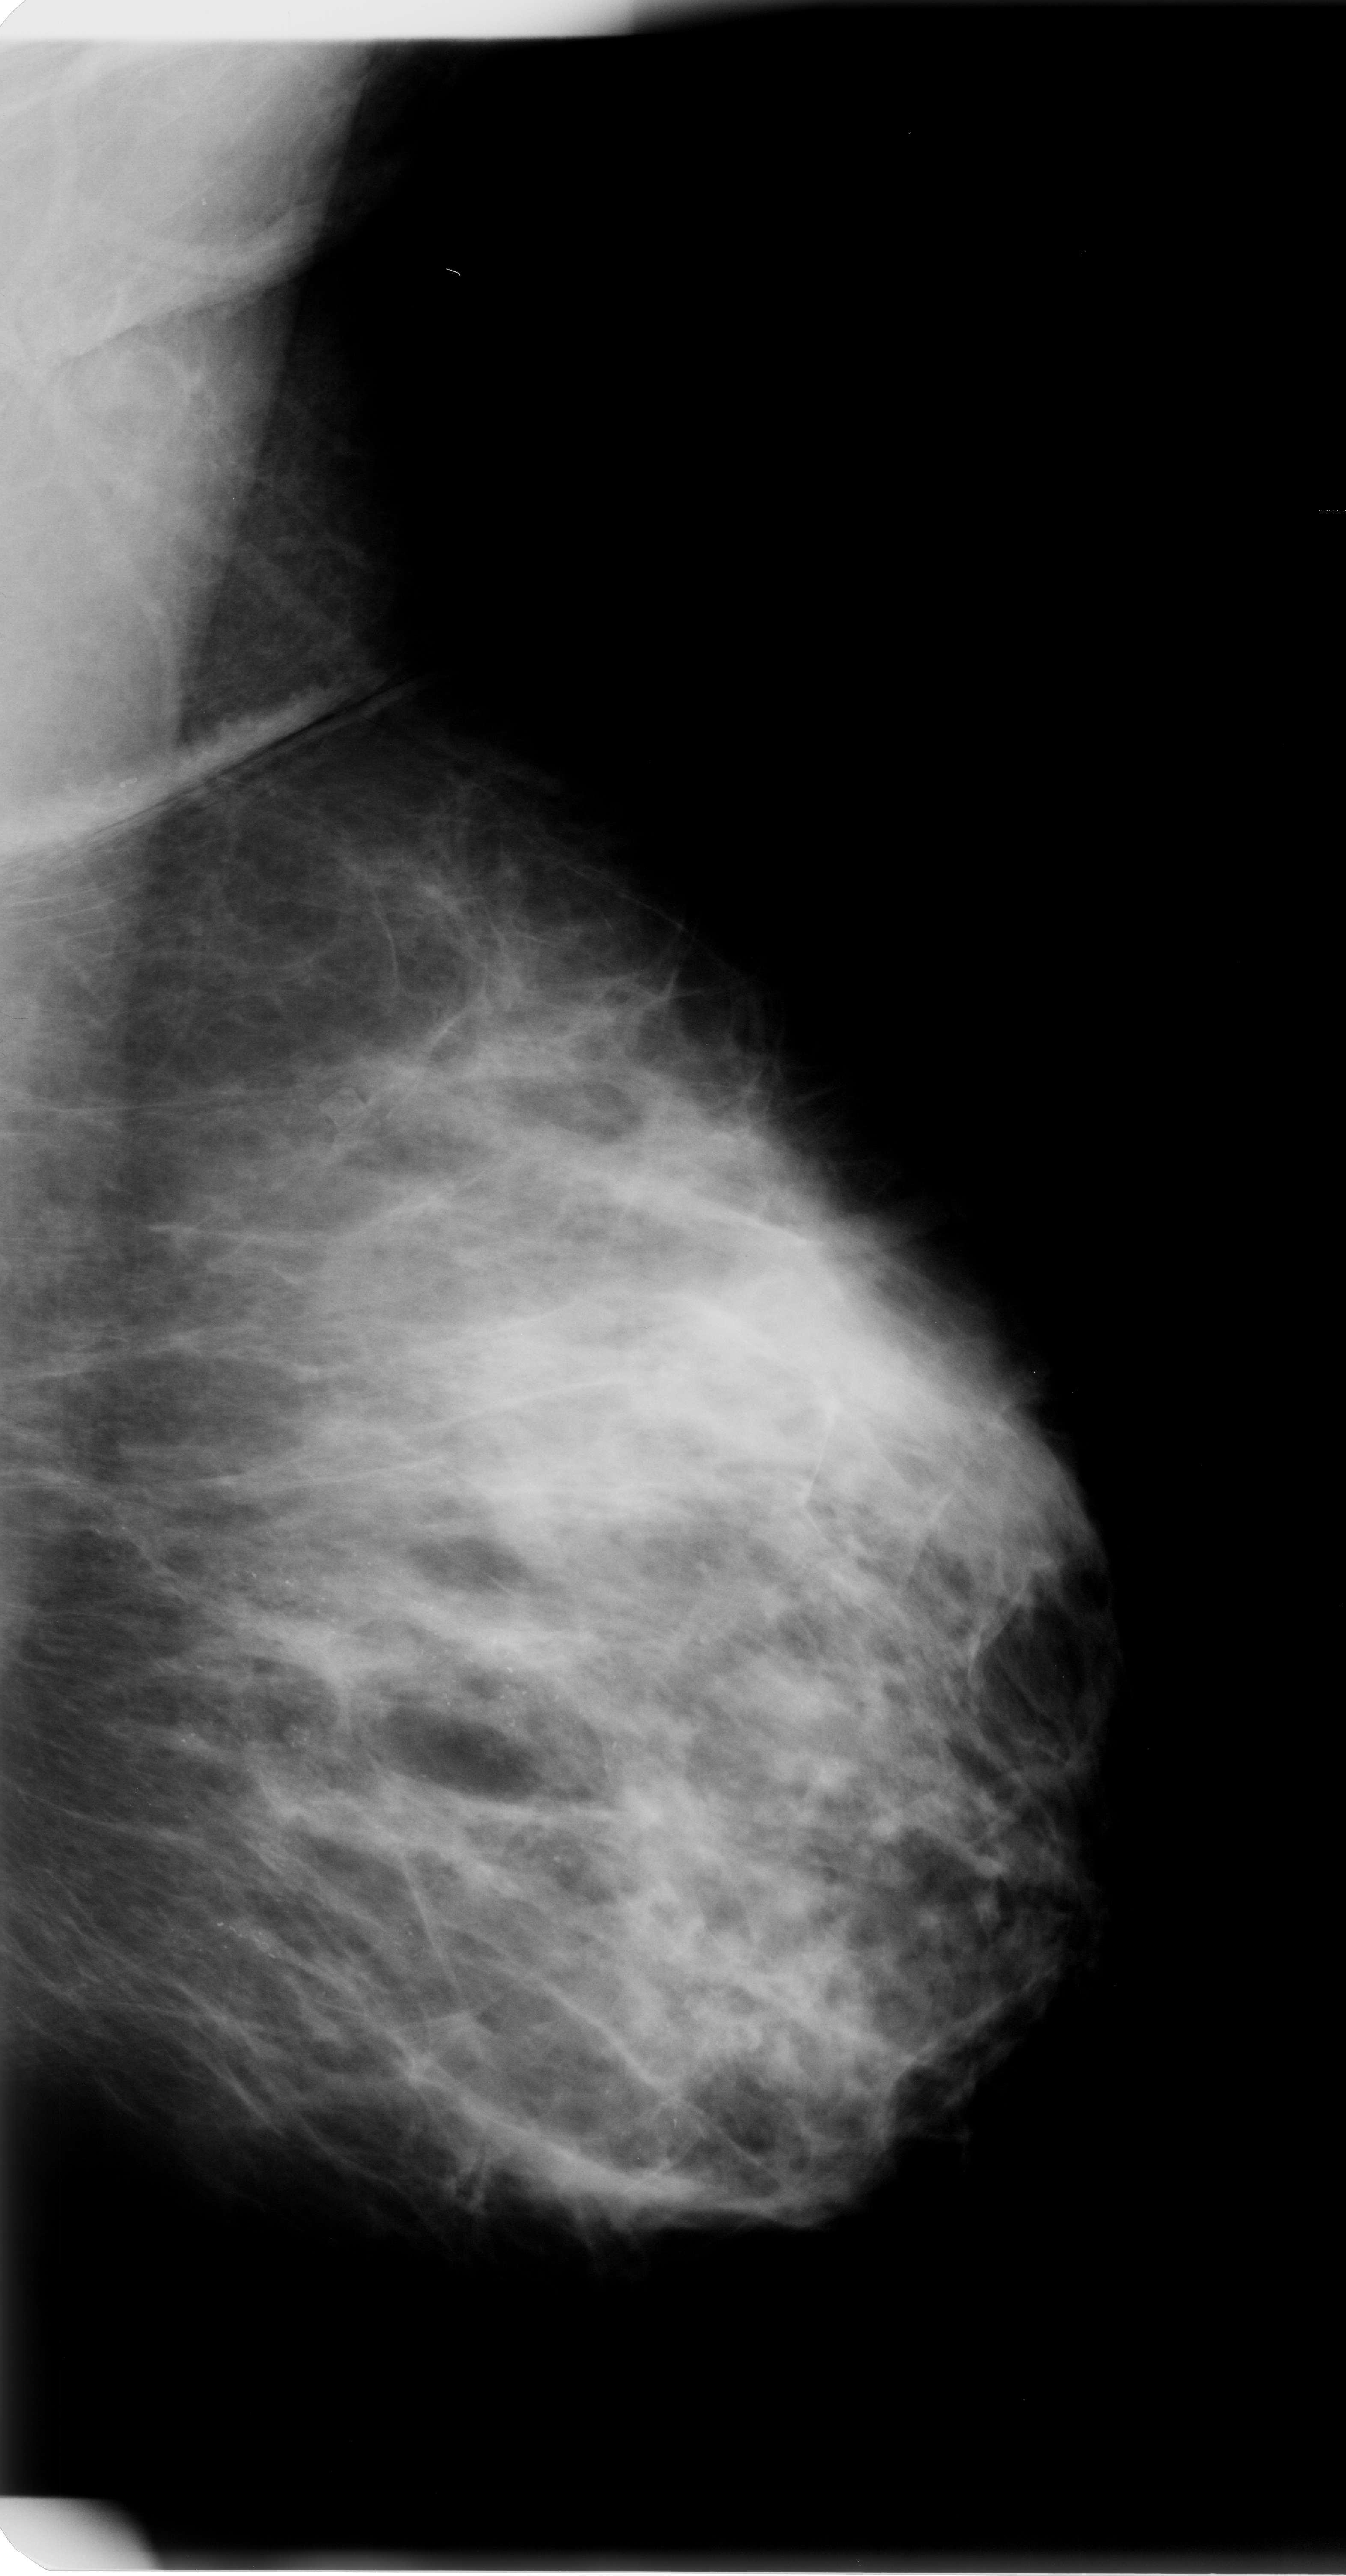
Mammogram (digitized film); left breast; MLO view; 1346 × 2576 image matrix.
Expert-marked regions of interest on this film, with their recorded descriptors:
- calcifications, morphology pleomorphic, distribution regional; BI-RADS assessment category 5; subtlety rating 5 on a 1 (subtle) to 5 (obvious) scale; pathology result (as recorded, not read from the image): malignant: bounding box <0,1404,980,2313> (left, top, right, bottom; pixels)